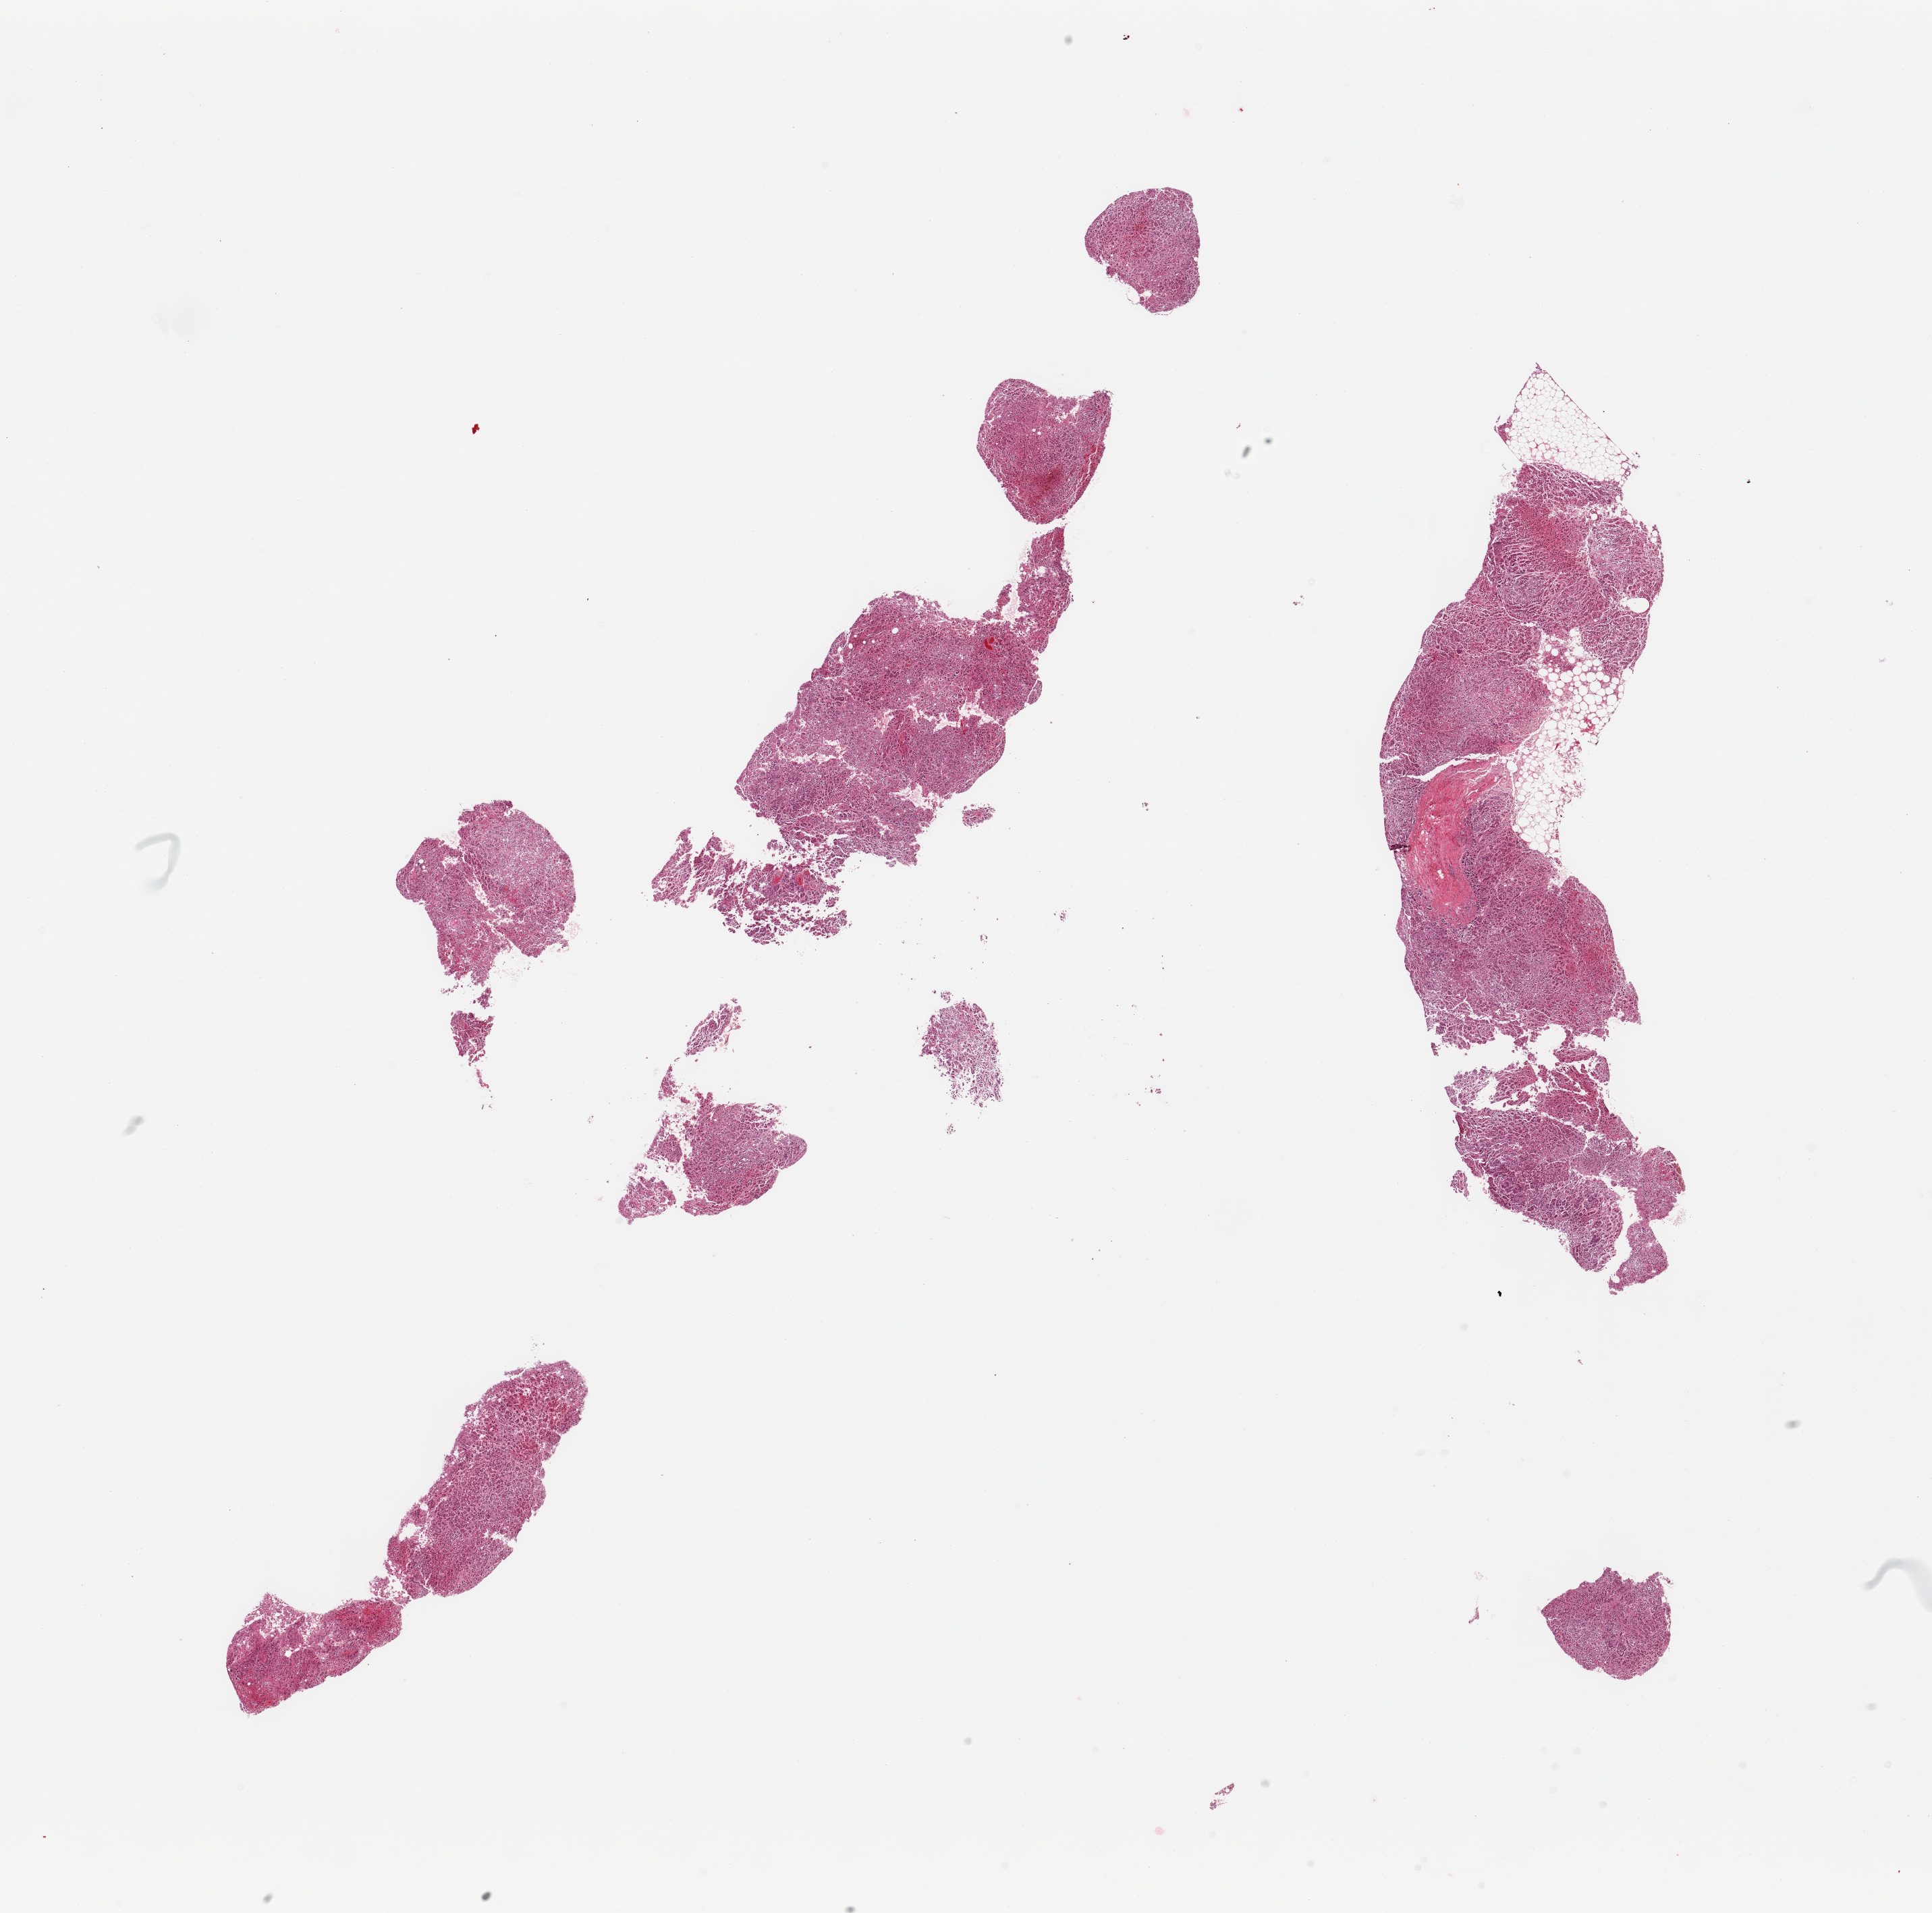
Digitized haematoxylin and eosin-stained section — shown as a low-resolution overview of the whole scanned area (about 22.6 x 22.4 mm); PAXgene-fixed, paraffin-embedded tissue; target tissue: adrenal gland; tissue donor sample.
Reviewer comment on this tissue sample: 2 pieces (fragemented), all cortex, ~10% adherent fat.